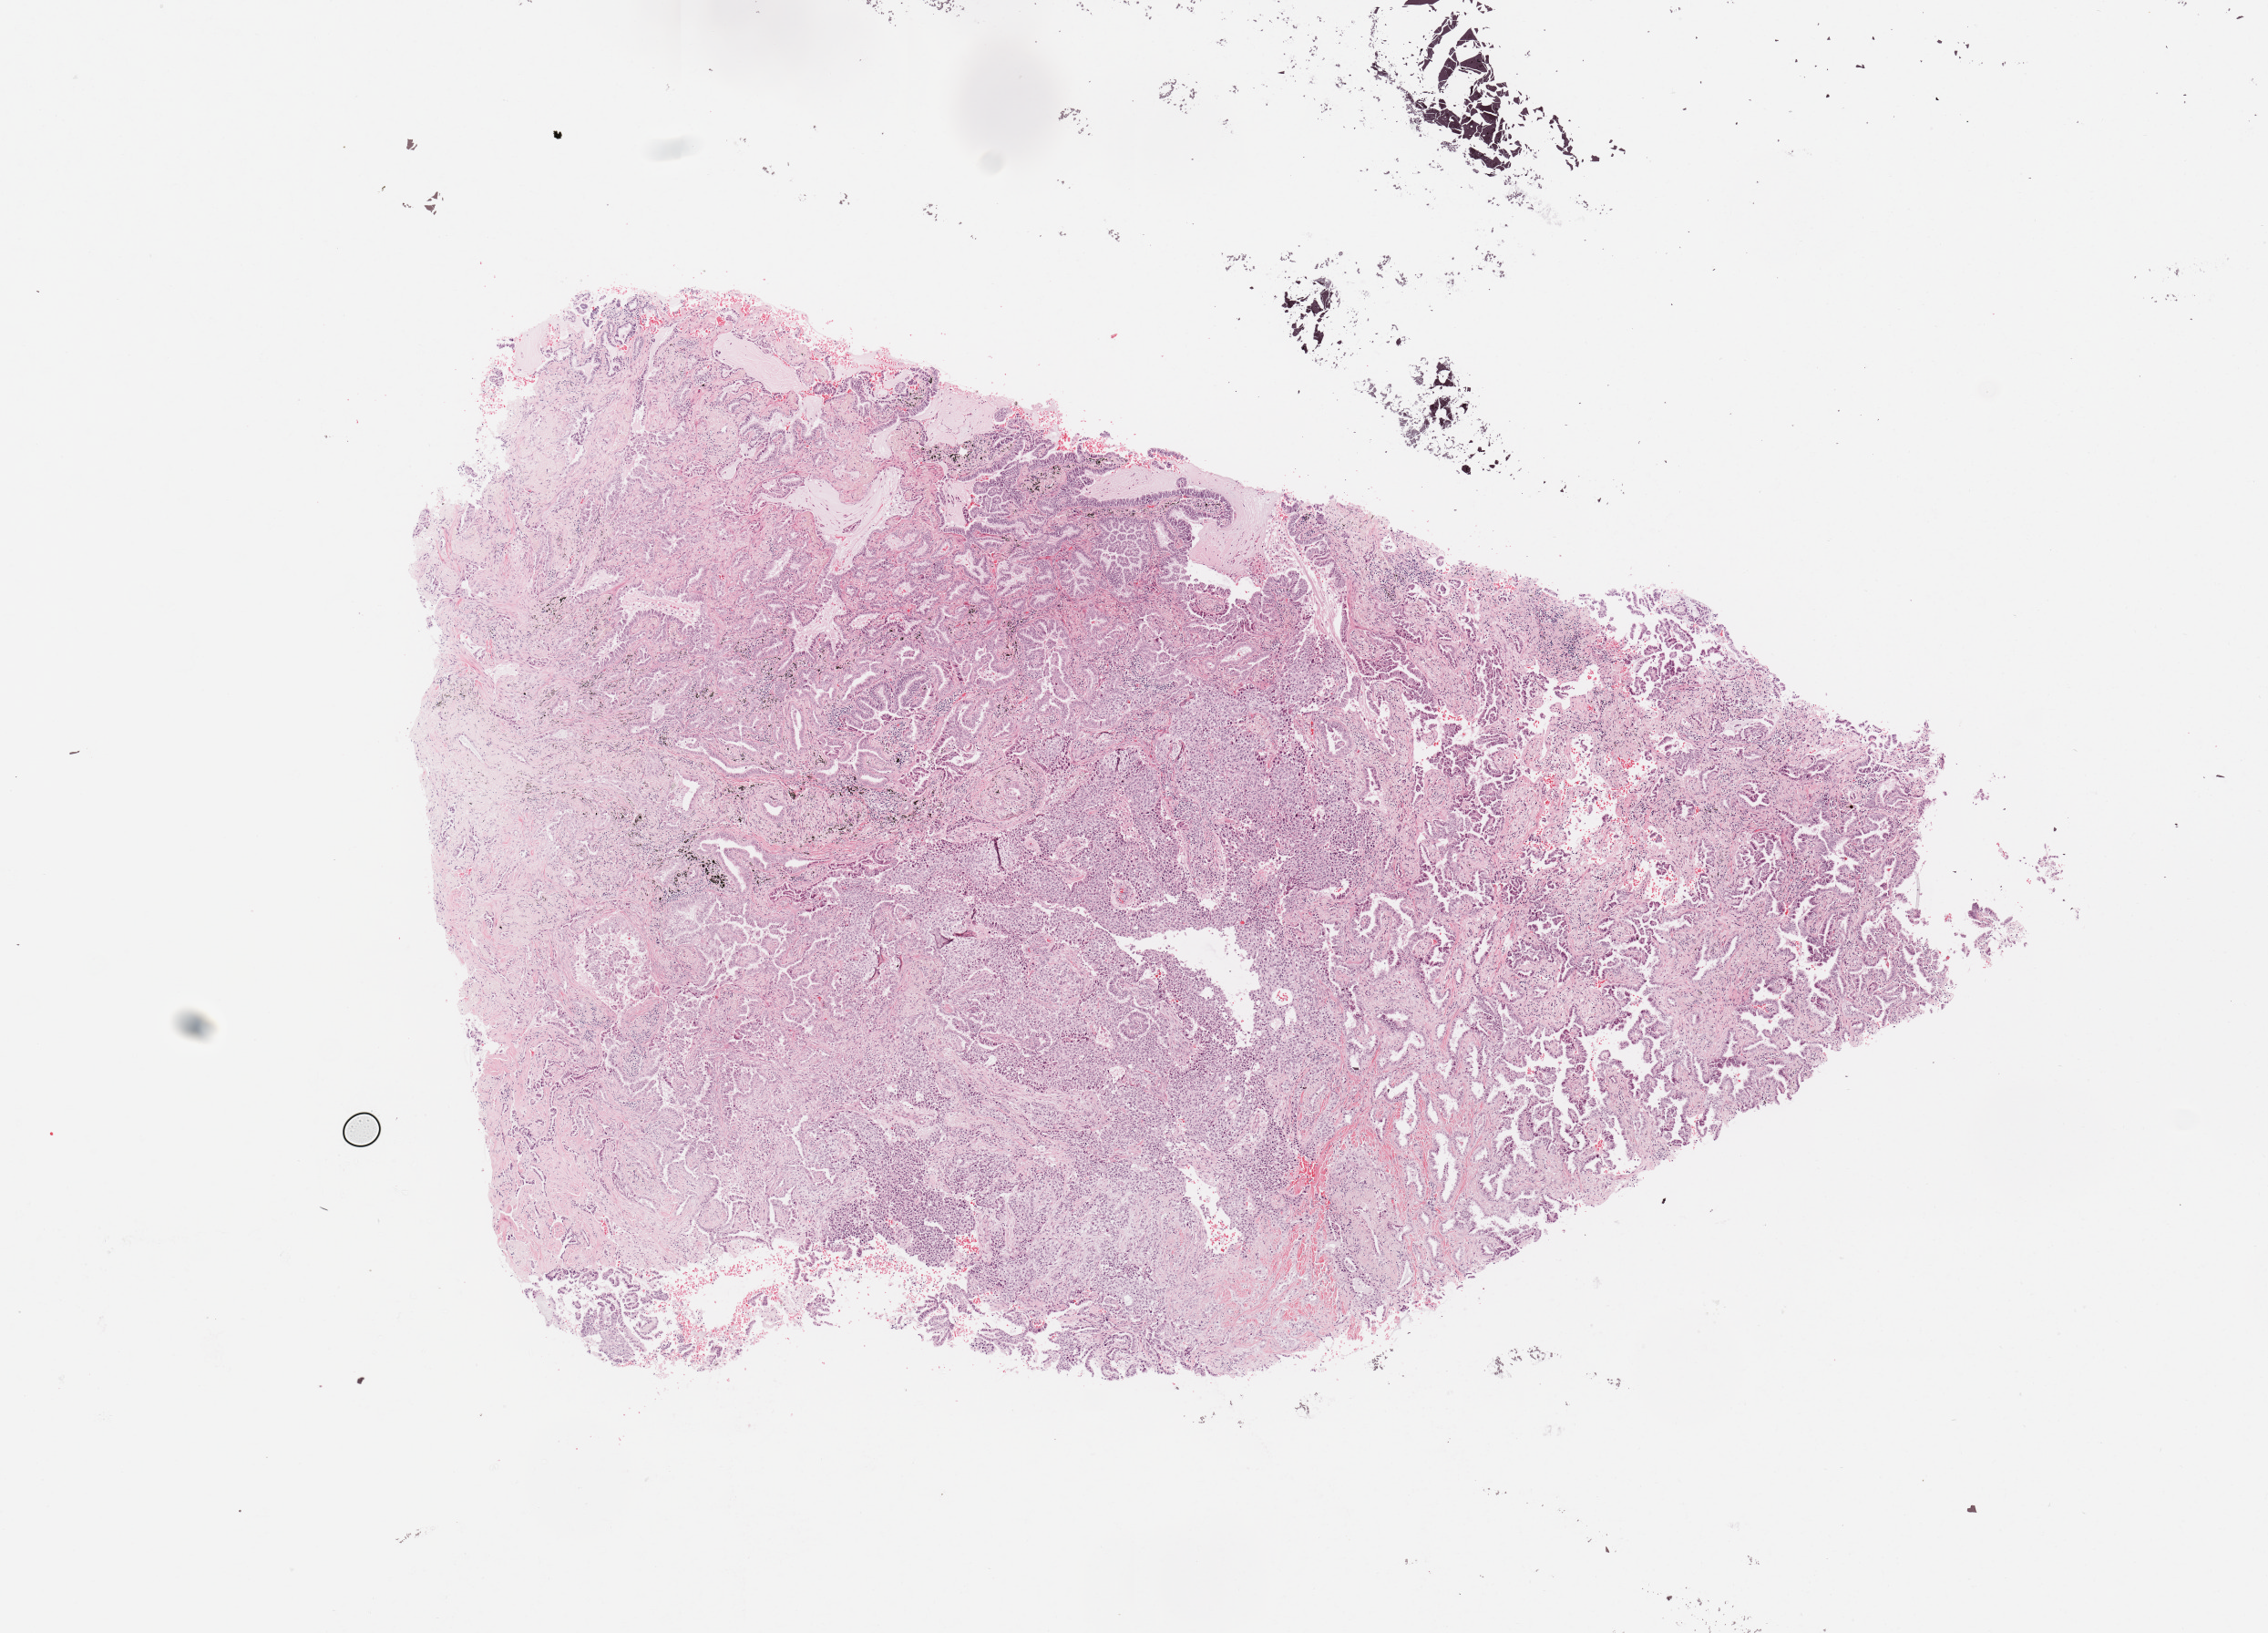
Whole-slide histology image, H&E — shown as a low-resolution overview of the whole scanned area (about 9.8 x 7.1 mm, acquisition: 20x scan). Tumour tissue sample, sampled site: lung. Patient: male, age 64 years. Histologic grade: G3 (poorly differentiated). Composition of this section per pathologist review: tumour nuclei 65%, necrosis 5%.
AJCC pathologic stage: IIB. Histologic diagnosis: Adenocarcinoma, NOS.